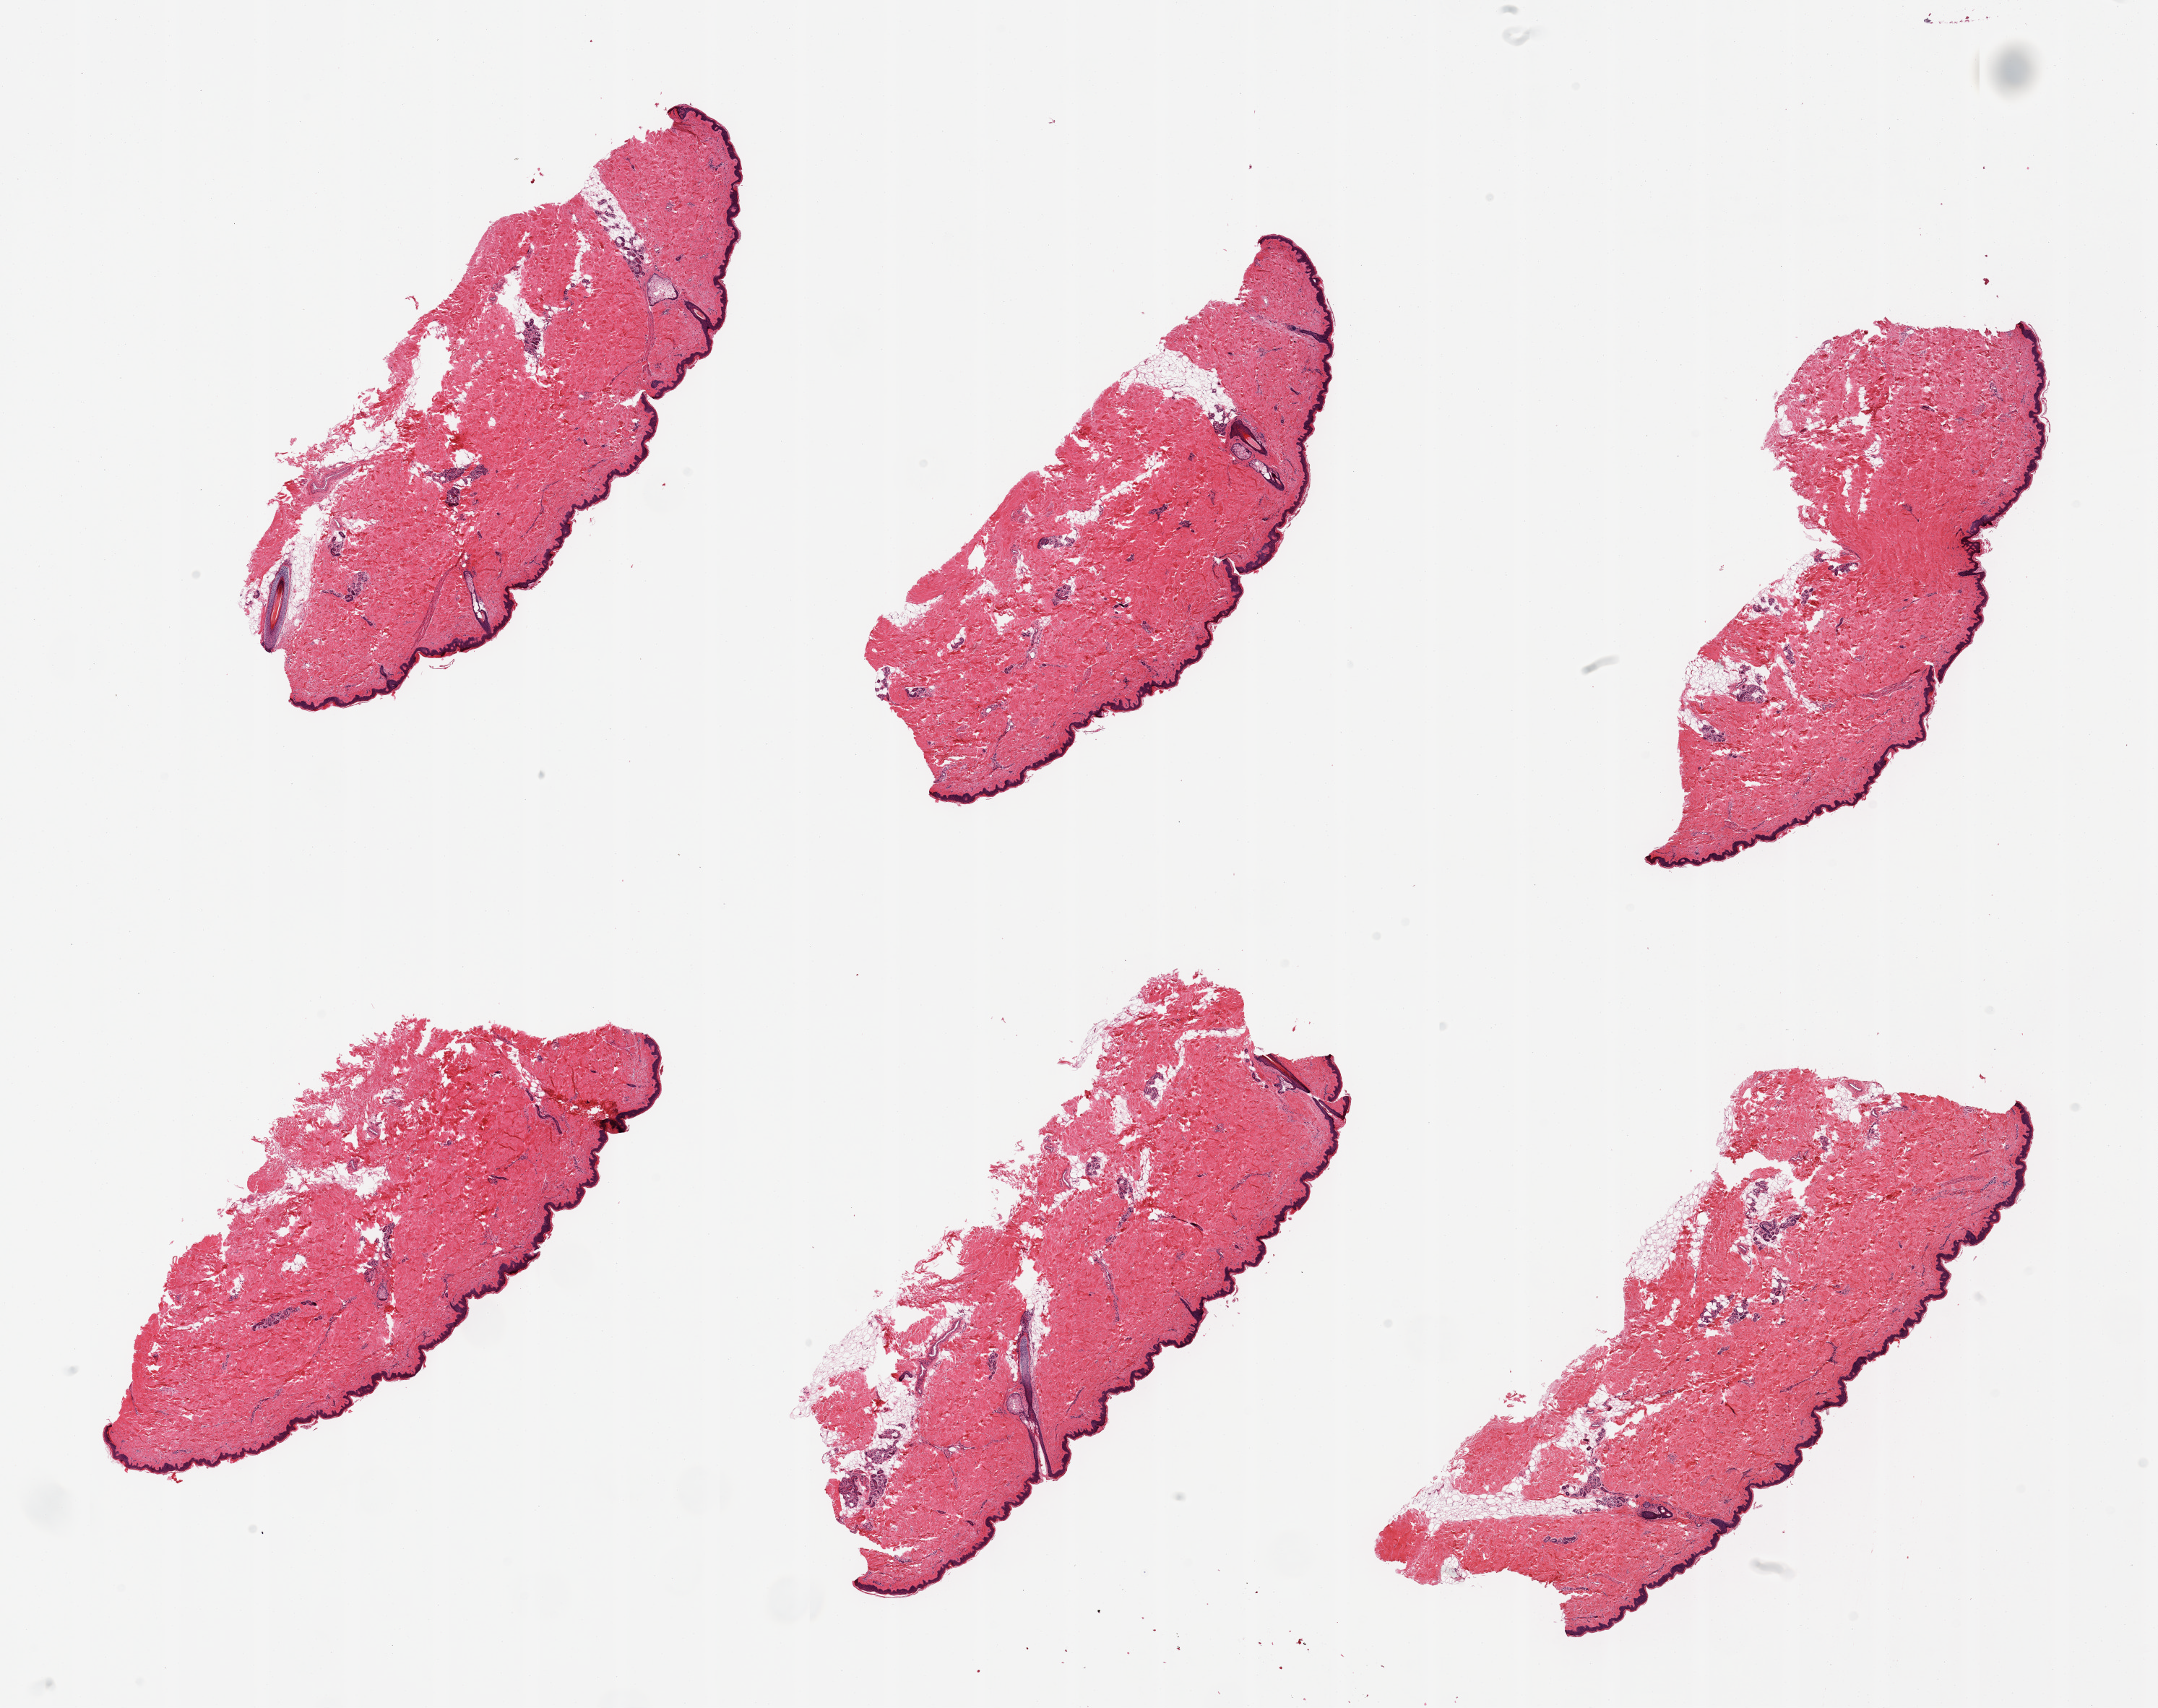
Whole-slide image, haematoxylin and eosin stain — low-resolution overview of the scanned area, about 23.6 x 18.7 mm (slide scanned at 20x), PAXgene-fixed paraffin-embedded (PFPE) section, target tissue: skin of lower leg, donor tissue sample. Donor: female.
Reviewer comment on this tissue sample: 6 pieces, minimal dermal fat; squamous epithelium is ~30-40 microns.